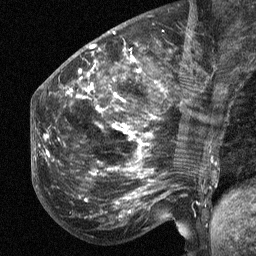
Breast MRI (dynamic contrast-enhanced), one sagittal slice. Position 23 of 64 along the scan axis. Dynamic contrast-enhanced study with each time point stored as its own series, time point 2 of 3 at this slice position (early post-contrast, ordered by acquisition time). 1.5 T. TE 4.8 ms, TR 27 ms. 2.3 mm slice thickness. 256 × 256 image matrix, field of view 200 × 200 mm. Female patient, age 50 years. From the clinical record (not read from this slice): setting: breast cancer imaged before/during neoadjuvant chemotherapy; receptor status: HER2-positive.
Outlined on this slice (semi-automatically segmented with operator editing):
- analysis volume of interest (the breast-tissue region the enhancement analysis was run in; not a lesion): bounding box [x1, y1, x2, y2] px = [53, 64, 211, 218]
- tumour enhancement mask (voxels above the 90 % enhancement threshold inside the analysis volume of interest): [67, 70, 156, 199]